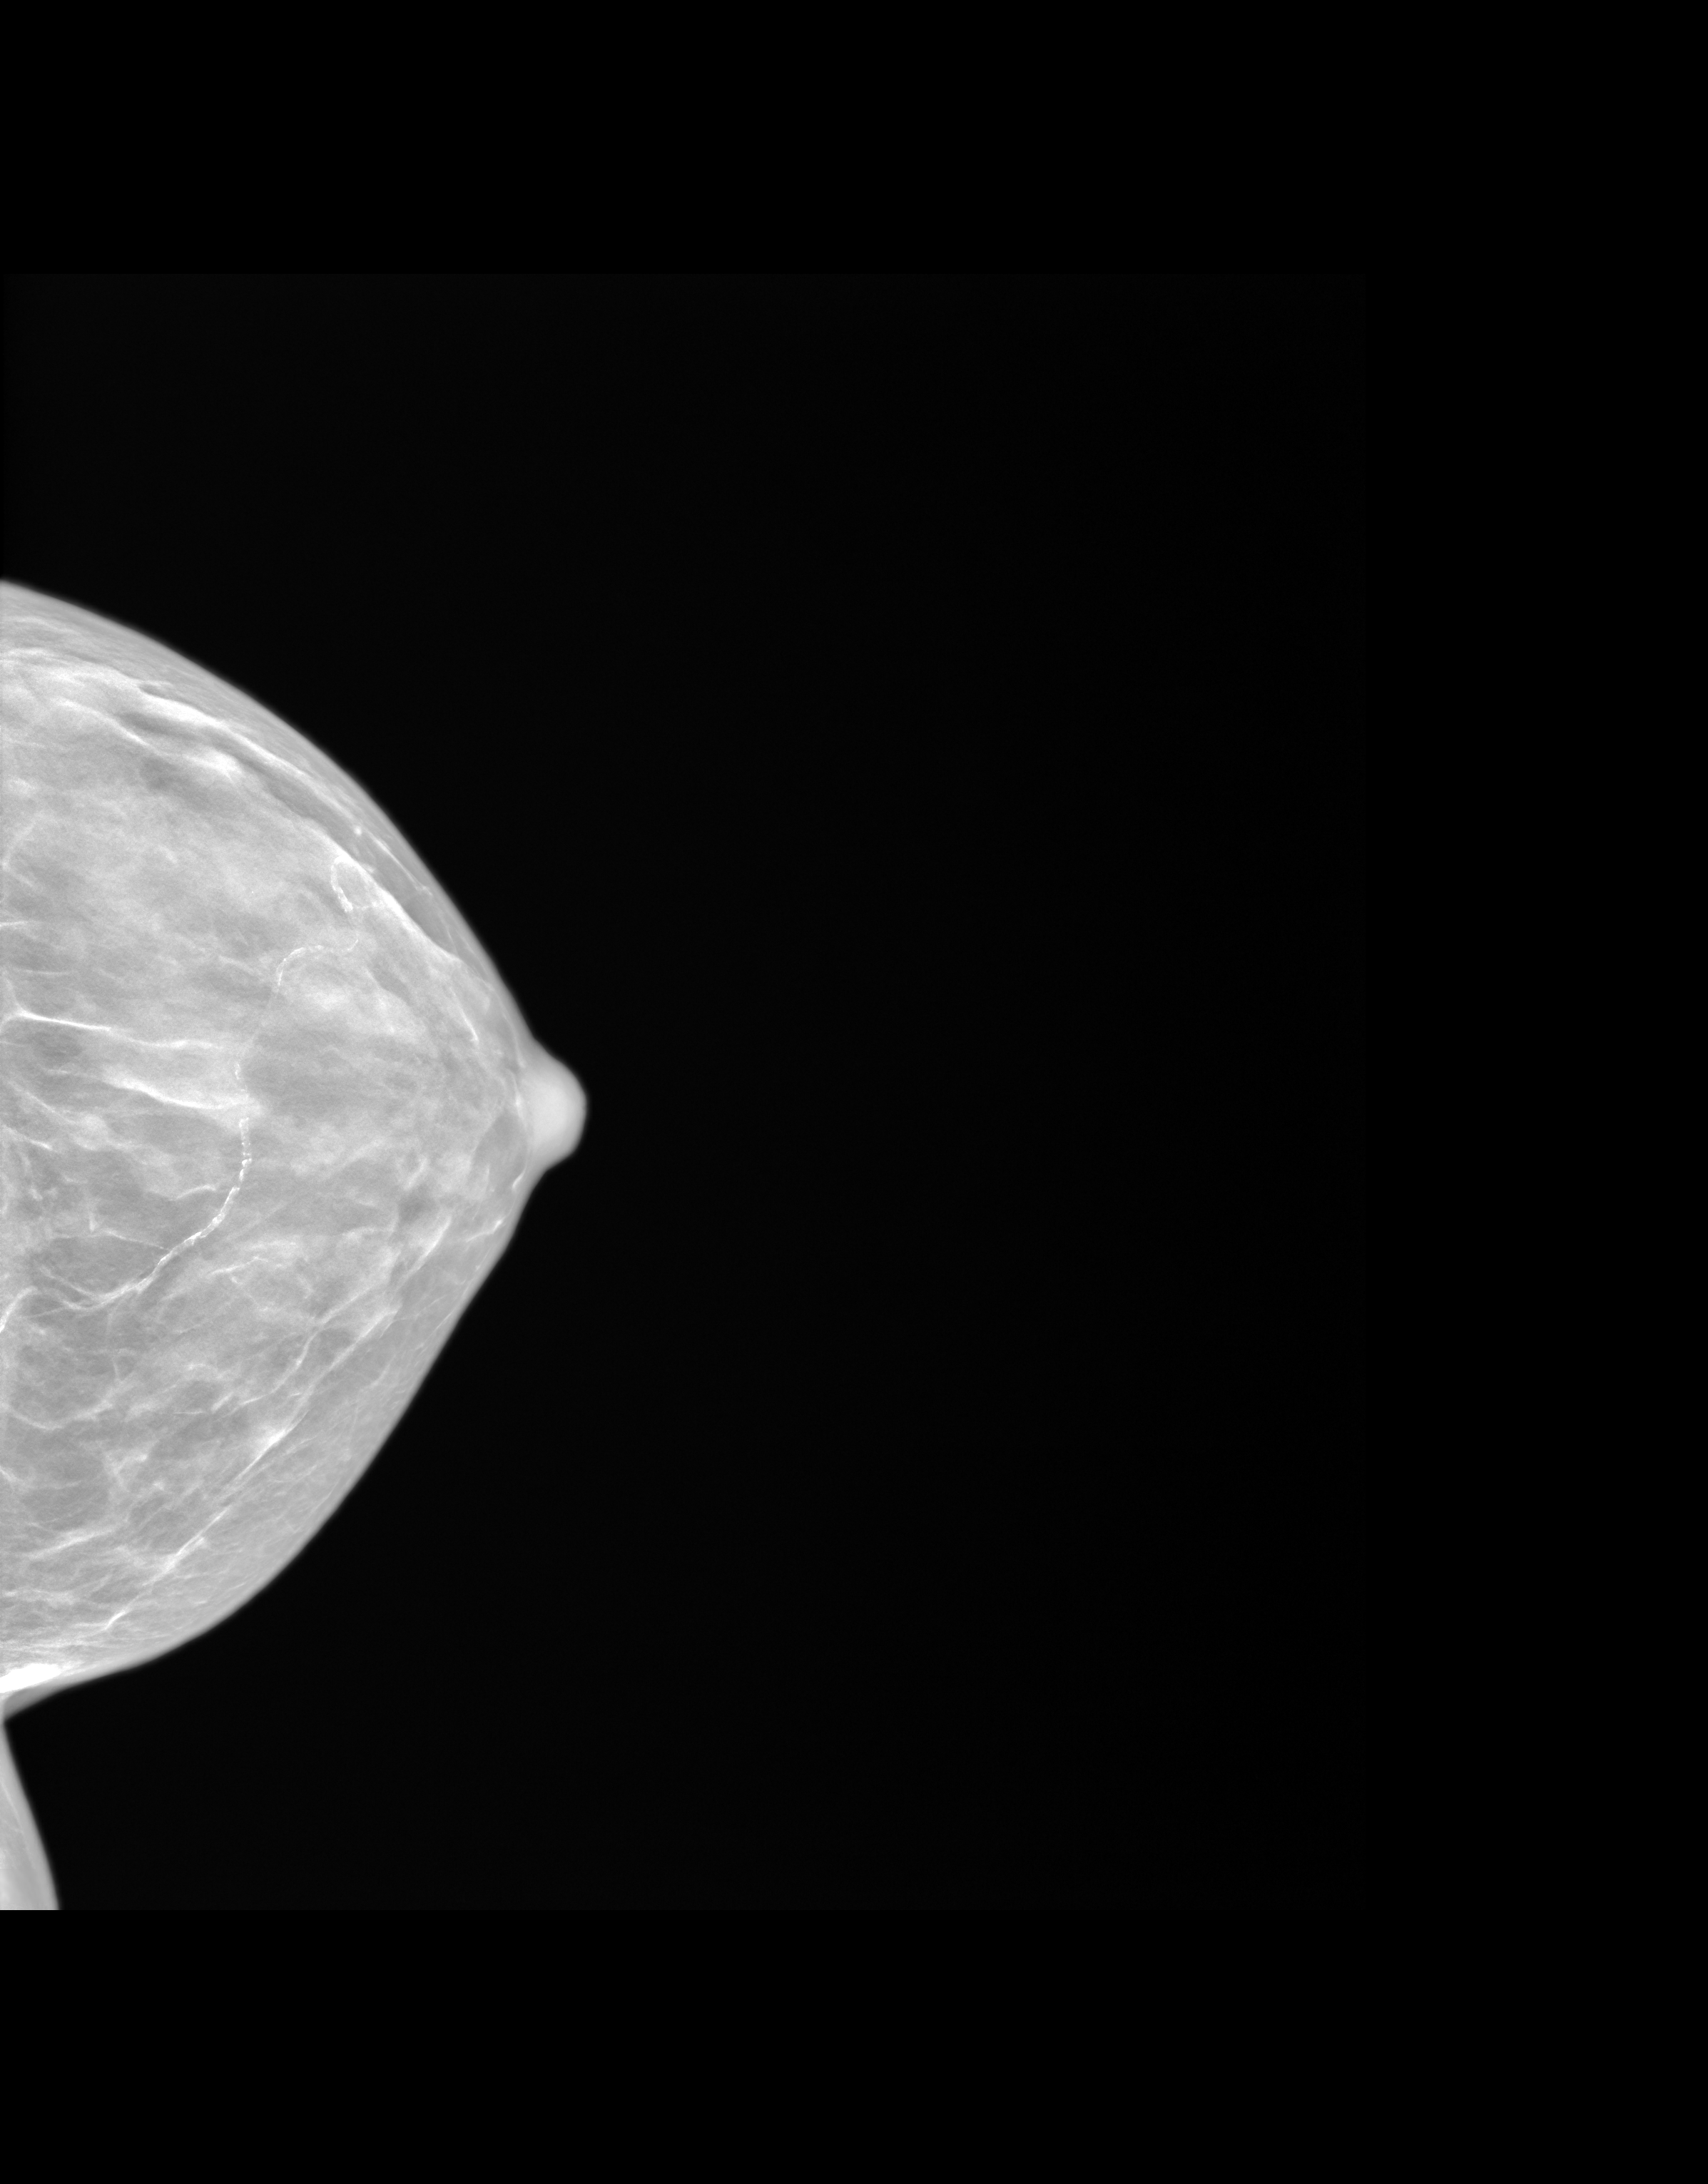
Screening examination. Patient: female, 60 years.
Image type: synthesized 2-D view from tomosynthesis. Breast: left. Projection: cranio-caudal projection.